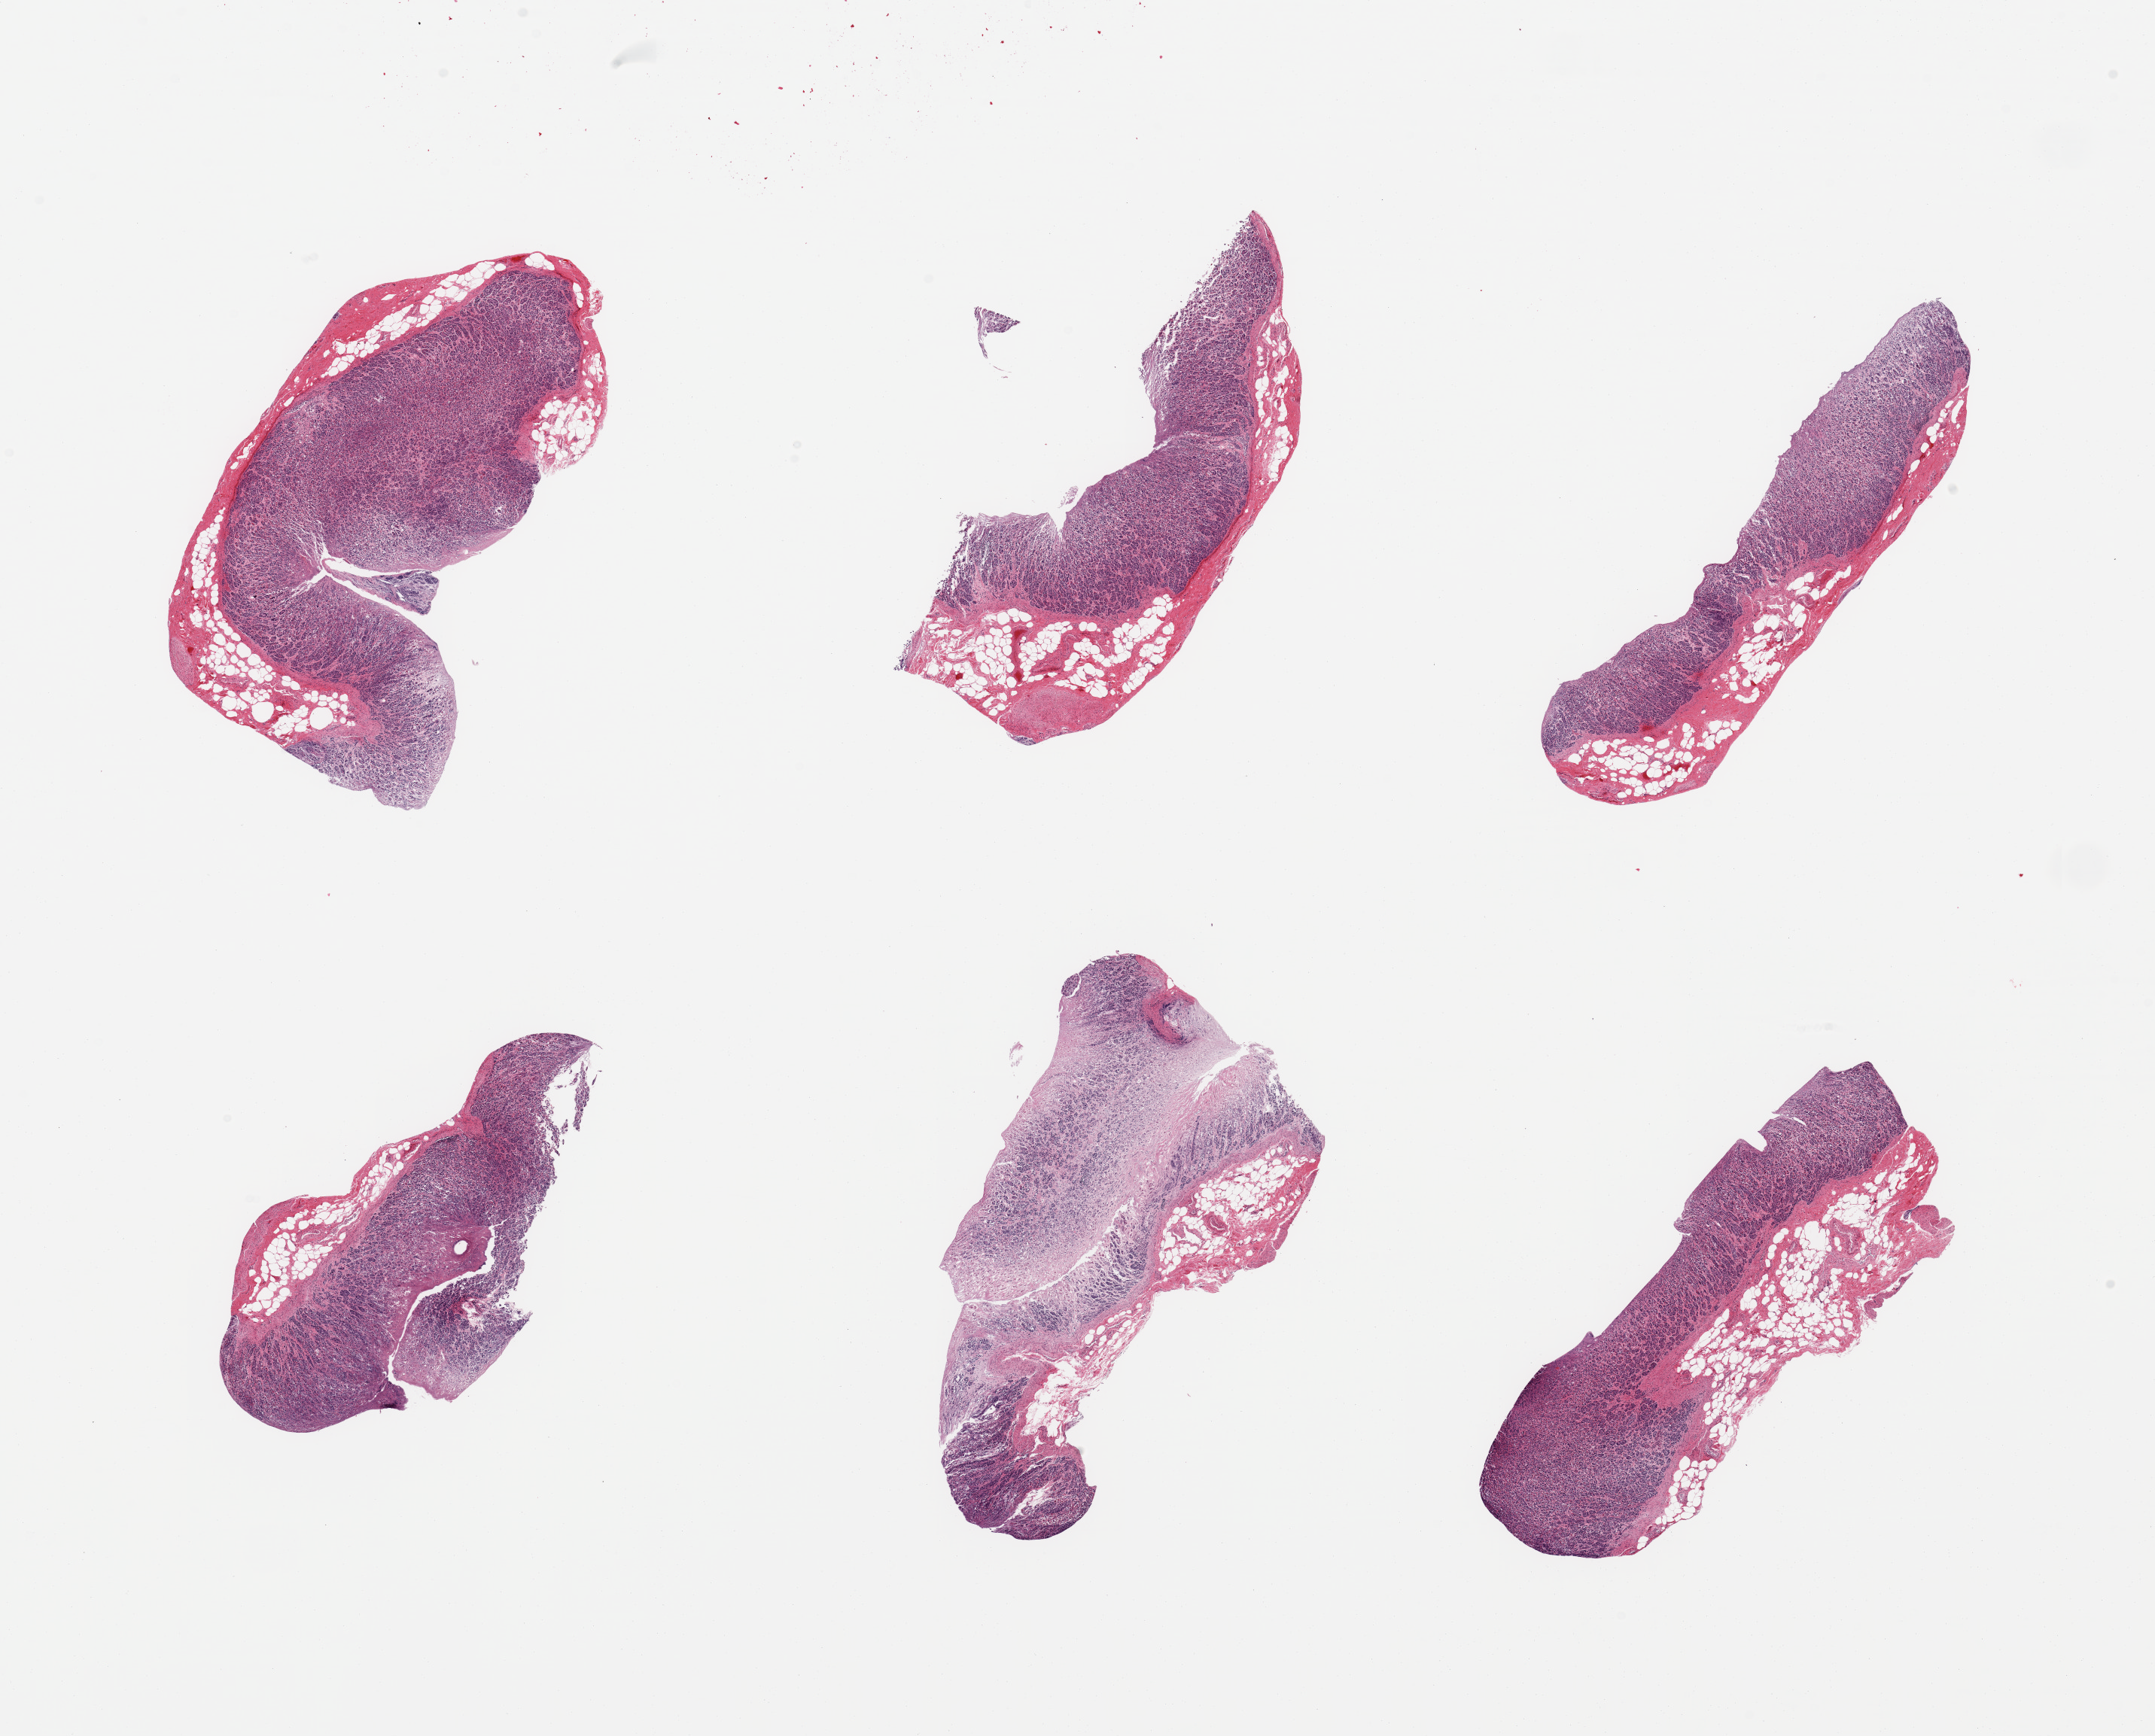
Haematoxylin and eosin whole-slide image, shown as a low-resolution overview of the whole scanned area (about 22.6 x 18.2 mm); PAXgene-fixed paraffin-embedded (PFPE) section; target tissue: stomach; tissue donor sample. Male donor.
Reviewer comment on this tissue sample: 6 pieces; predominantly mucosa with minimal muscularis, moderate to severe autolysis.